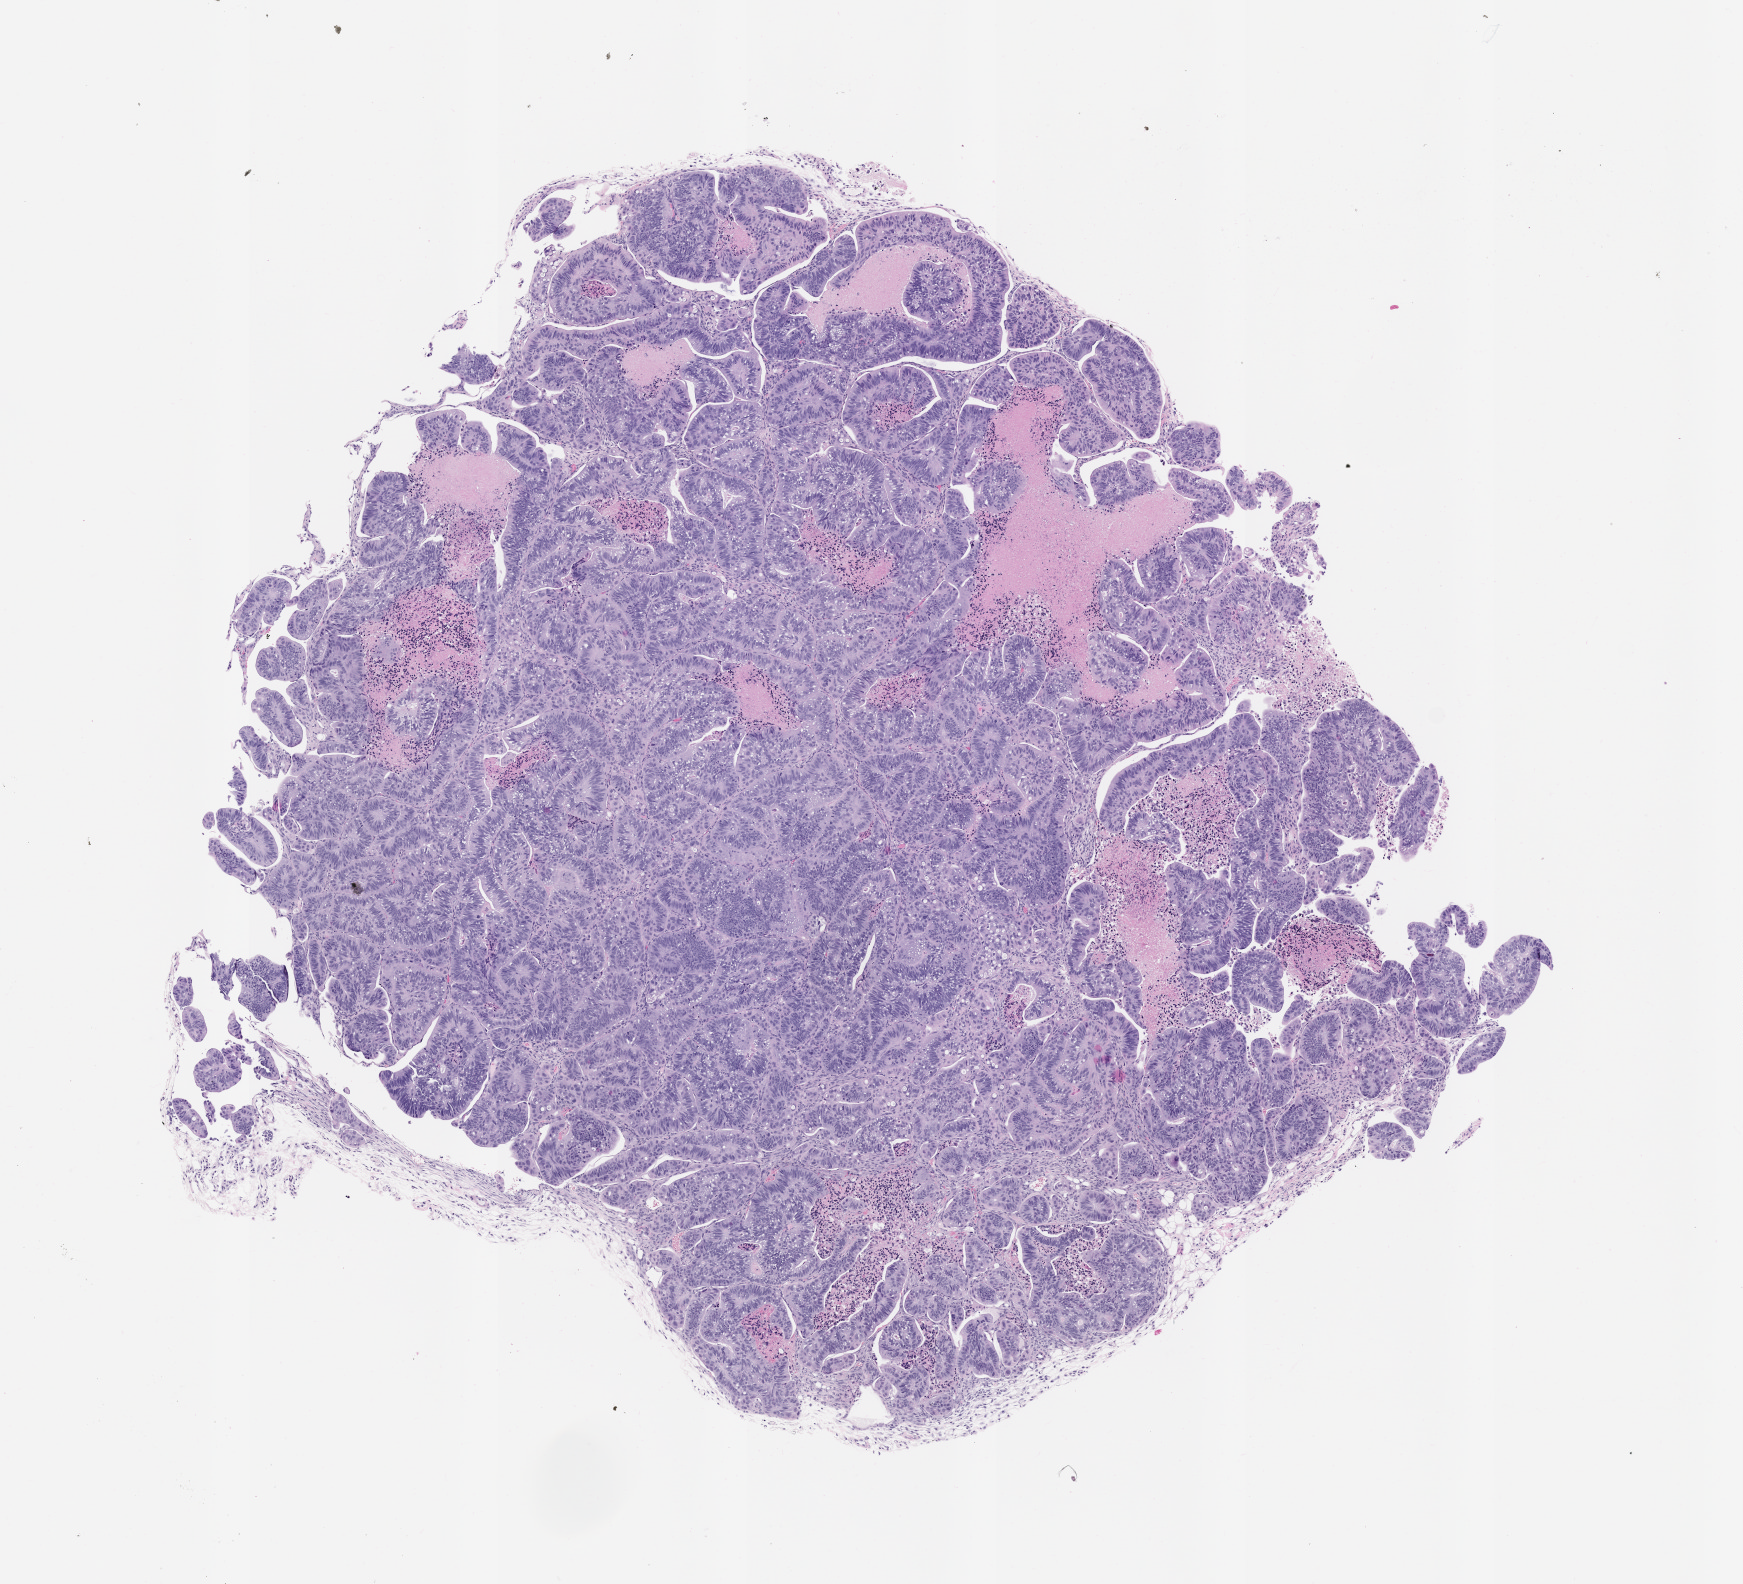
Whole-slide image, hematoxylin and eosin (H&E): patient-derived xenograft (human tumor grown in a mouse), passage 2, shown as a low-resolution overview of the whole scanned area (about 7.0 x 6.4 mm); formalin-fixed, paraffin-embedded (FFPE) tissue; tumor site category: colon.
* originating patient diagnosis: Colon Adenocarcinoma